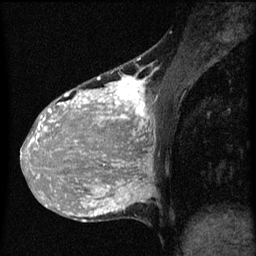
Breast MRI (dynamic contrast-enhanced), one sagittal slice; dynamic contrast-enhanced series, image 2 of 3 at this slice position (ordered by acquisition); 1.5 T; TE 4.2 ms, TR 8 ms; 2 mm slice thickness; 256 × 256 image matrix. Female patient, age 36 years.
Outlined on this slice (semi-automatic segmentation, software-assisted and operator-edited):
- analysis volume of interest (the breast-tissue region the enhancement analysis was run in; not a lesion): bounding box <32,68,161,161> (left, top, right, bottom; pixels)
- tumour enhancement mask (voxels above the 70 % enhancement threshold inside the analysis volume of interest): <32,78,151,161>